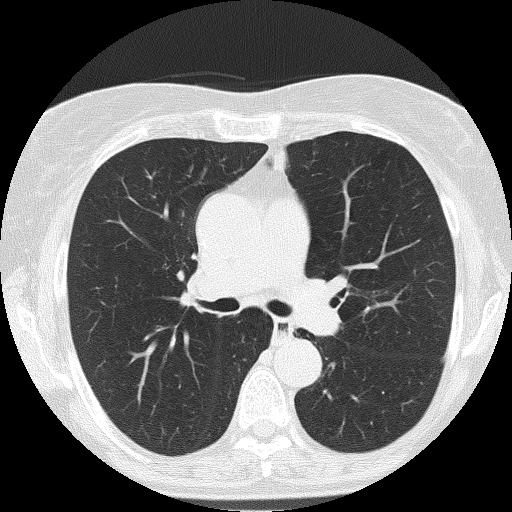
Low-dose screening chest CT, one axial slice; position 107 of 166 along the scan axis; reconstruction kernel FC51; 120 kVp; lung window (W 1500 / L -600 HU); 2 mm slice thickness; 512 × 512 image matrix.
Outlined on this slice (manually delineated by an expert):
- lesion 2 (nodule, upper lobe of left lung): bounding box (x1, y1, x2, y2) in pixels: (274, 151, 286, 173)